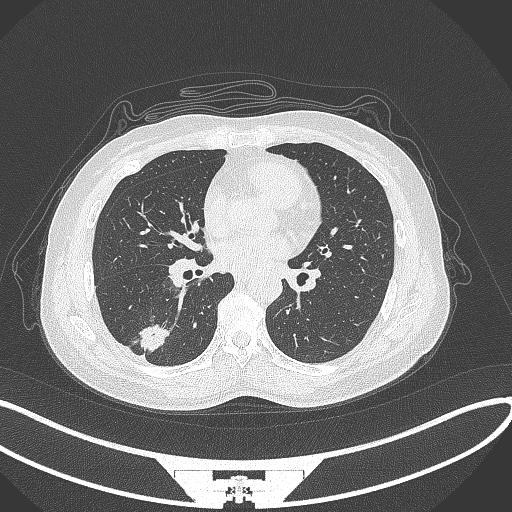
Chest CT, one axial slice. Slice 139 of 352 in the series (ordered by position). Reconstruction kernel B70f. 120 kVp. Lung window (W 1500 / L -600 HU). 1 mm slice thickness. 512 × 512 image matrix, field of view 400 × 400 mm. Patient: female, 55 years. Case-level facts recorded for this patient, not image findings: clinical TNM (as recorded): T1c N1 M0.
Structures marked on this image (rectangle marked by the reading radiologist):
- lung tumour (recorded histology: adenocarcinoma): bounding box [x1, y1, x2, y2] px = [136, 319, 173, 356]